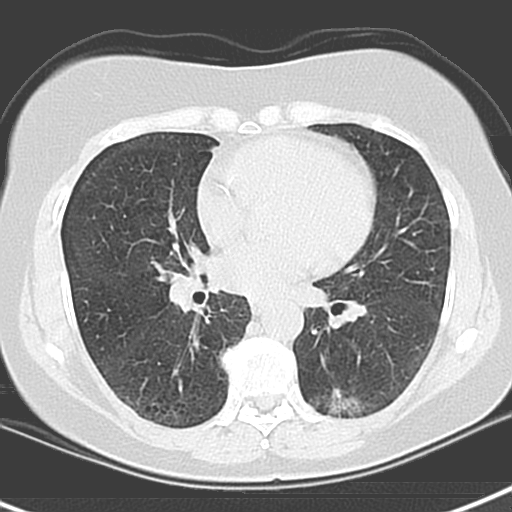
Axial slice from a low-dose chest CT screening exam. First (baseline) screen. Lung window (W 1500 / L -600 HU). 3.2 mm slice thickness. Slice 75 of 129 in the series. 512 × 512 image matrix. Female, age 55 years at enrolment. Current smoker at enrolment.
Expert-annotated lung lesion, bounding box [x1, y1, x2, y2] px = [313, 374, 389, 423]. The screening reader recorded 3 non-calcified nodules or masses ≥4 mm on this exam (left upper lobe, left lower lobe, left lower lobe); which of them this box marks is not recorded. Official screen result: positive, change unspecified: nodule(s) >= 4 mm or enlarging nodule(s), mass(es), or other non-specific abnormalities suspicious for lung cancer. Lung cancer was diagnosed 1063 days after this screen: adenocarcinoma with mixed subtypes, left lower lobe, poorly differentiated (G3), stage IA (AJCC 6th edition), 21 mm at pathology.